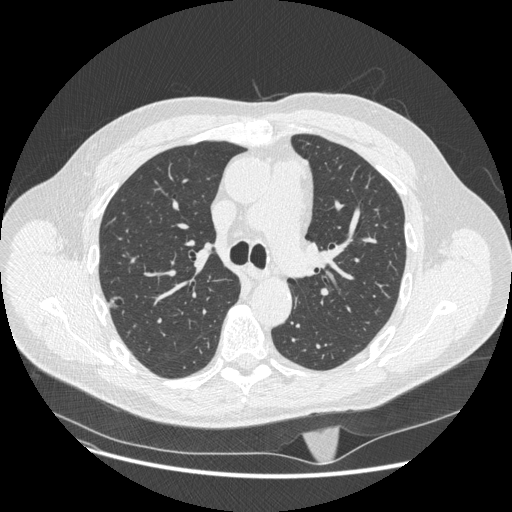
Axial slice from a low-dose chest CT screening exam; second screening round (one year after baseline); lung window (W 1500 / L -600 HU); standard (soft-tissue) reconstruction kernel (STANDARD); slice 78 of 247 in the series. Male, age 62 years at enrolment. Current smoker at enrolment.
Expert-annotated lung lesion, bounding box <97,288,132,317> (left, top, right, bottom; pixels). Reader record for this screening exam (exam-level; its link to the box is not recorded): non-calcified nodule or mass ≥4 mm, right upper lobe, 11 × 7 mm, smooth margins, pre-existing on the prior screen: yes. Later outcome: lung cancer diagnosed 482 days after this screen — adenocarcinoma, NOS, right upper lobe, moderately differentiated (G2), stage IA (AJCC 6th edition), 12 mm at pathology.